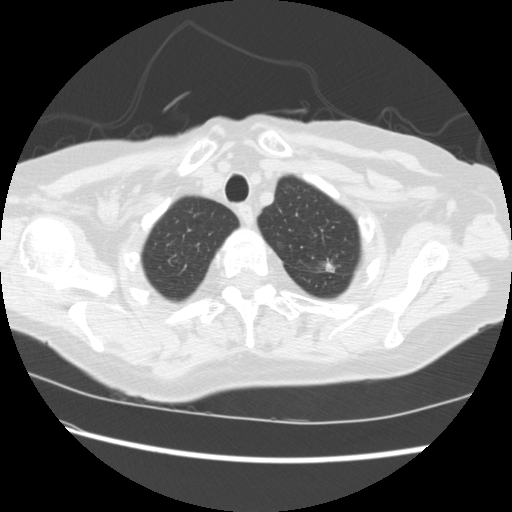
Chest CT (low-dose screening protocol), one axial image; baseline screening round; lung window (W 1500 / L -600 HU); standard (soft-tissue) reconstruction kernel (STANDARD); slice 33 of 224 in the series; 512 × 512 image matrix. Female, age 74 years at enrolment.
Expert reader's lesion annotation, box from (x=298, y=249) to (x=348, y=285) px. The screening reader recorded 2 non-calcified nodules or masses ≥4 mm on this exam (left upper lobe, right lower lobe); which of them this box marks is not recorded. Official screen result: positive, change unspecified: nodule(s) >= 4 mm or enlarging nodule(s), mass(es), or other non-specific abnormalities suspicious for lung cancer.